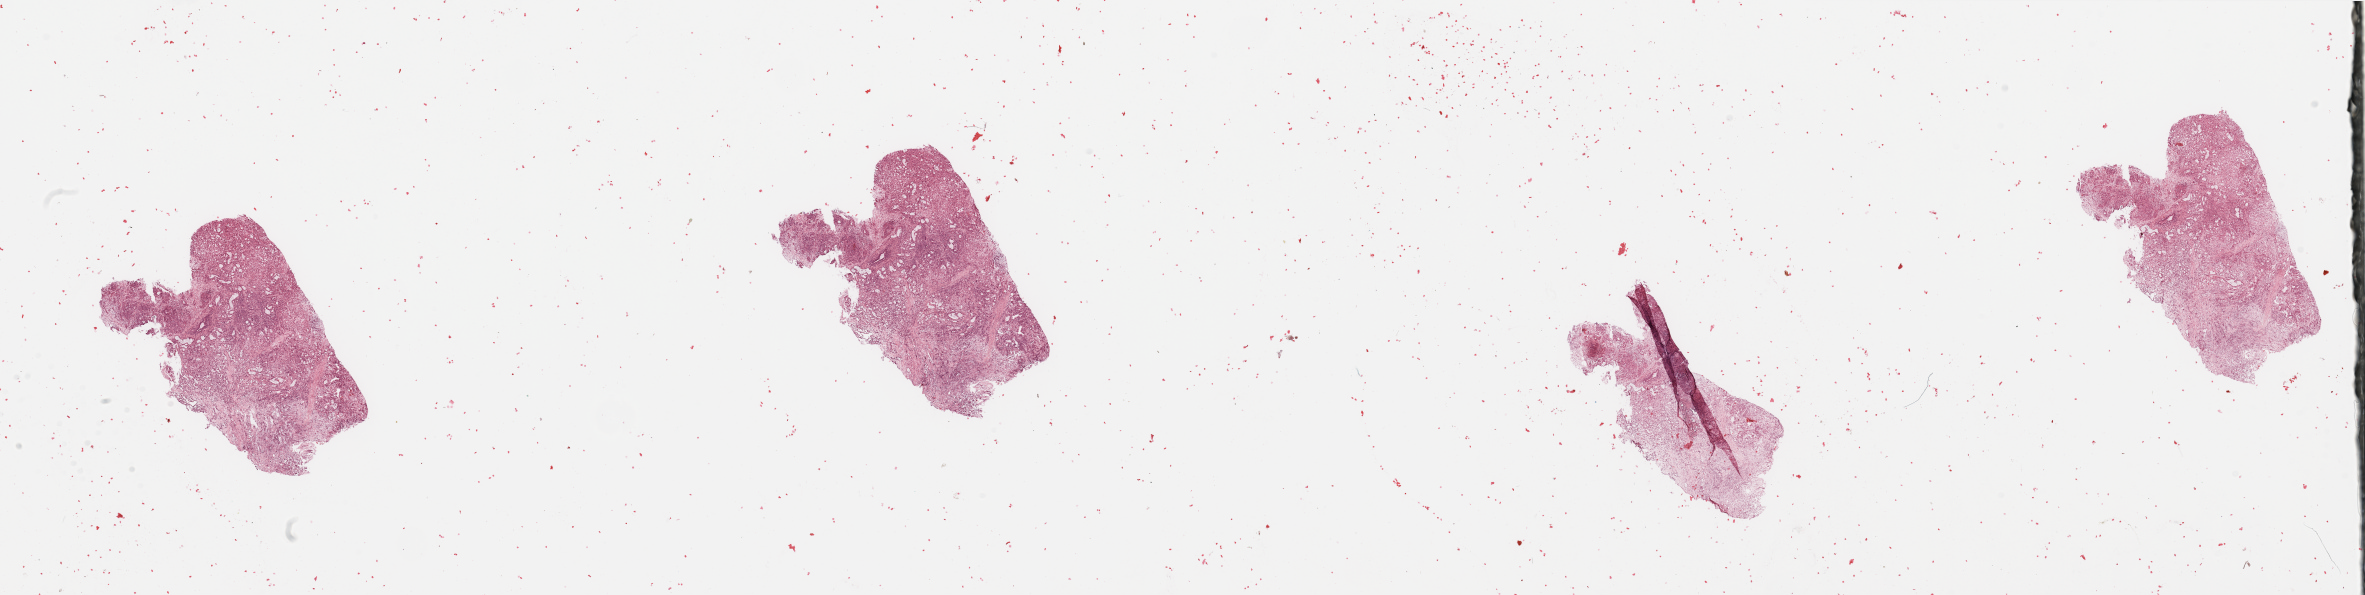
Digitized Hematoxylin and eosin (H&E) stained tissue section (whole slide), low-resolution overview of the scanned area, about 37.4 x 9.4 mm, tumour tissue sample, sampled site: pancreas. Patient: male, age 50 years. Histologic grade: G3 (poorly differentiated). Pathologist review of this section (percent, as recorded): tumour nuclei 80%, necrosis 5%.
Primary tumour site (as recorded): head. Diagnosis: Infiltrating duct carcinoma, NOS. AJCC pathologic stage: IV.